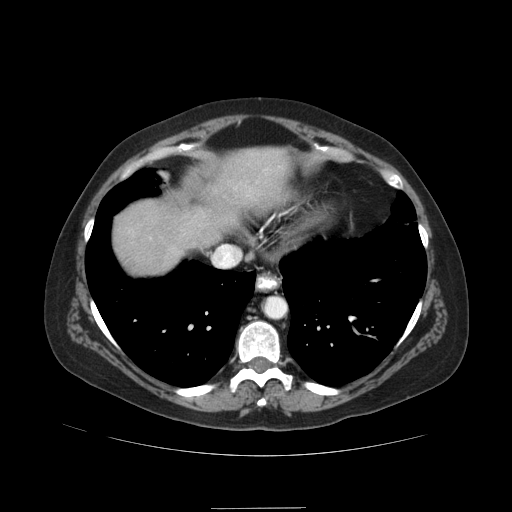
Contrast-enhanced abdominal CT (liver protocol), one axial slice; slice 78 of 89 in the series (ordered by position); reconstruction kernel STANDARD; 120 kVp; soft-tissue window (W 400 / L 40 HU); 2.5 mm slice thickness; 512 × 512 image matrix. Case-level facts recorded for this patient, not image findings: diagnosis: hepatocellular carcinoma (patient treated with transarterial chemoembolisation; whether this scan precedes or follows treatment is not stated here); TNM stage (as recorded): Stage-IIIB; Child-Pugh class: A.
Structures marked on this image (semi-automatically segmented with operator editing):
- liver parenchyma outside the tumour (the mass and vessels are separate outlines, so this box may not span the whole liver): box from (x=112, y=148) to (x=290, y=274) px